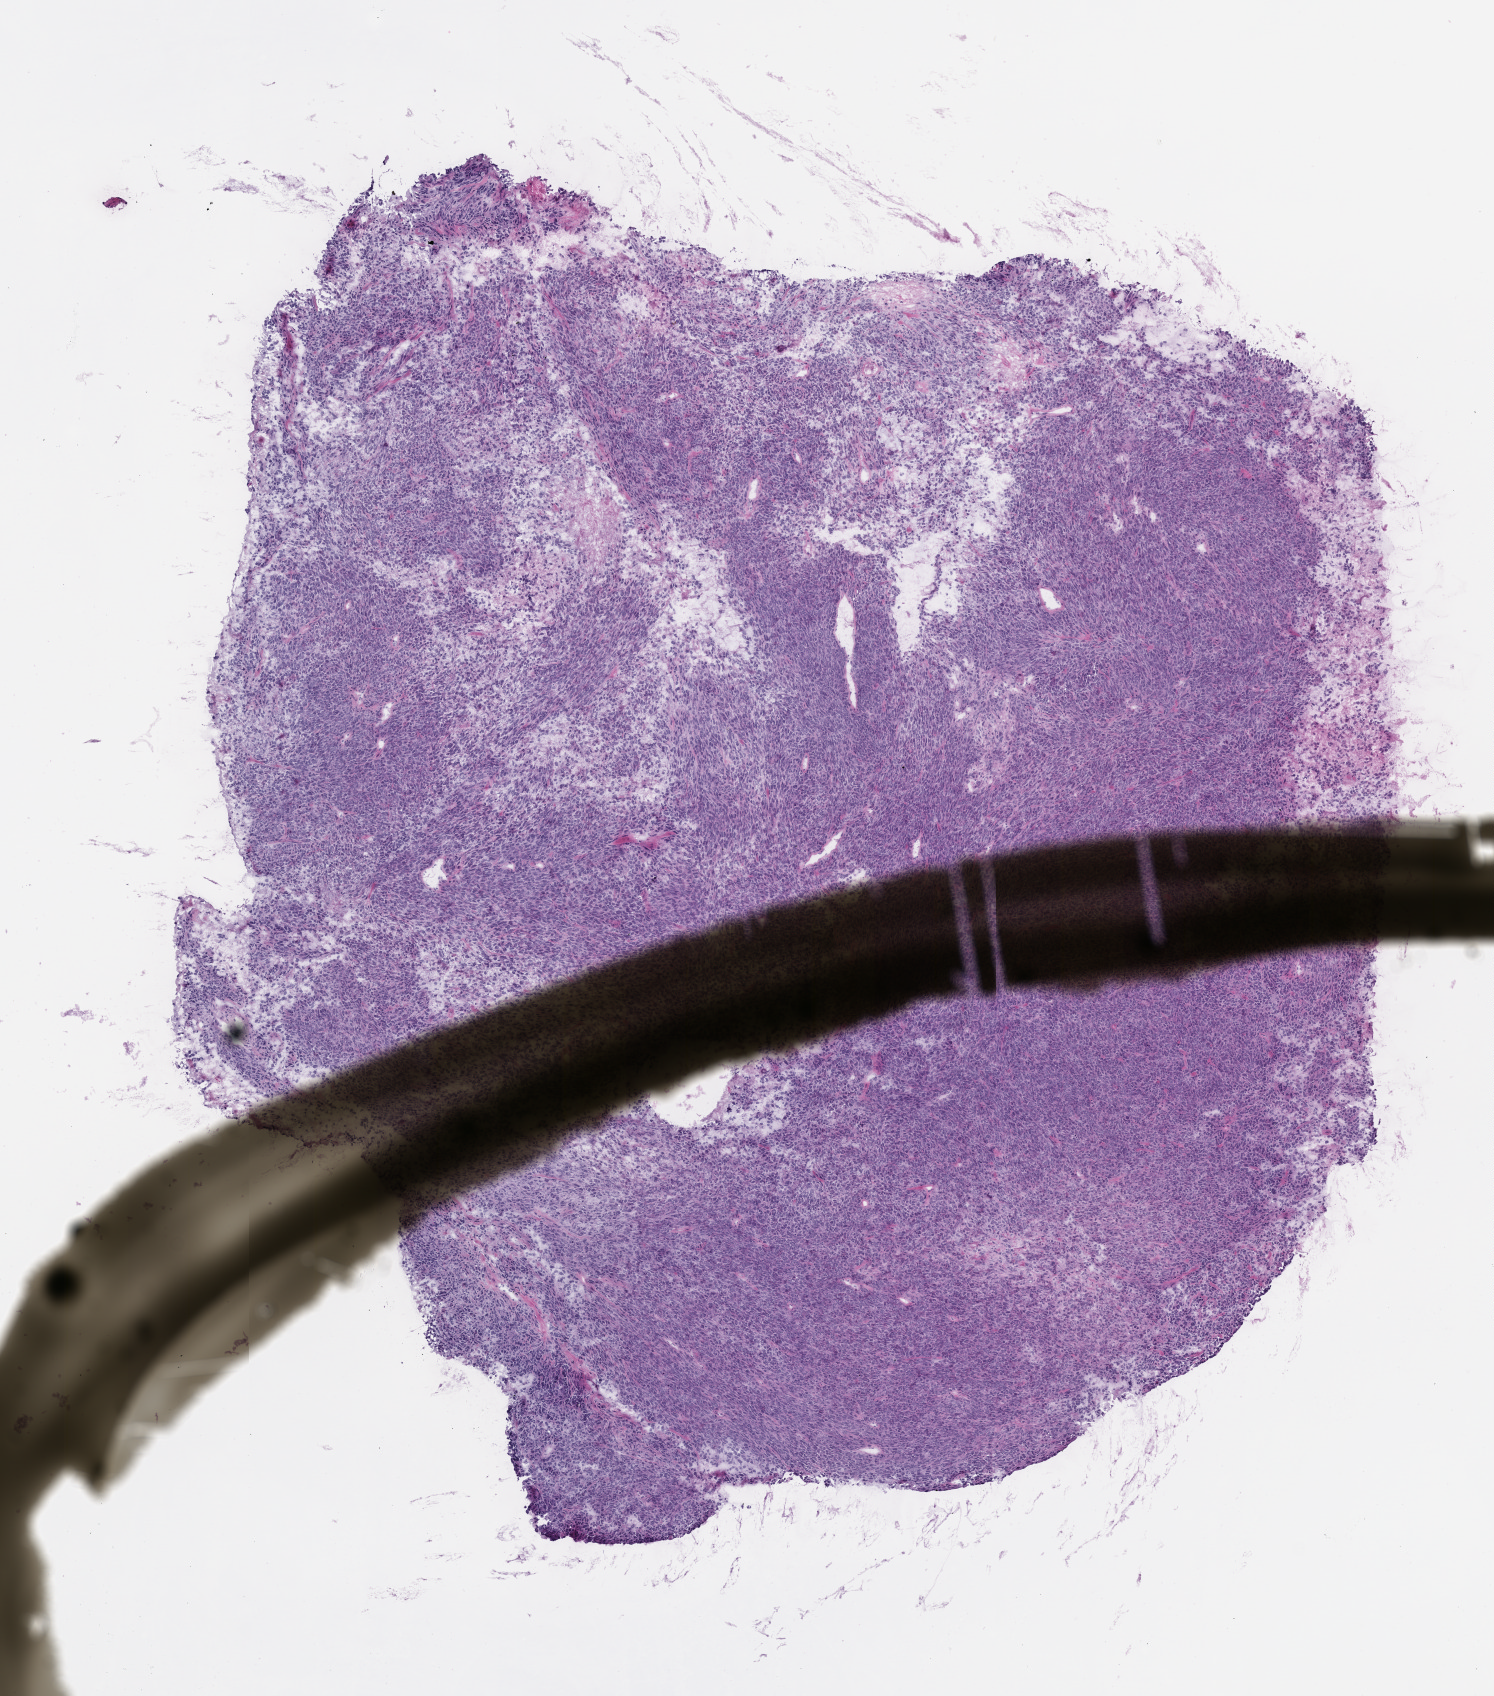
Whole-slide image, haematoxylin and eosin: patient-derived xenograft (human tumor grown in a mouse), passage 2 — whole scanned area (about 6.0 x 6.8 mm) shown as a low-resolution overview; formalin-fixed paraffin-embedded section; tumor site category: musculoskeletal.
- originating patient diagnosis: Spindle Cell Sarcoma